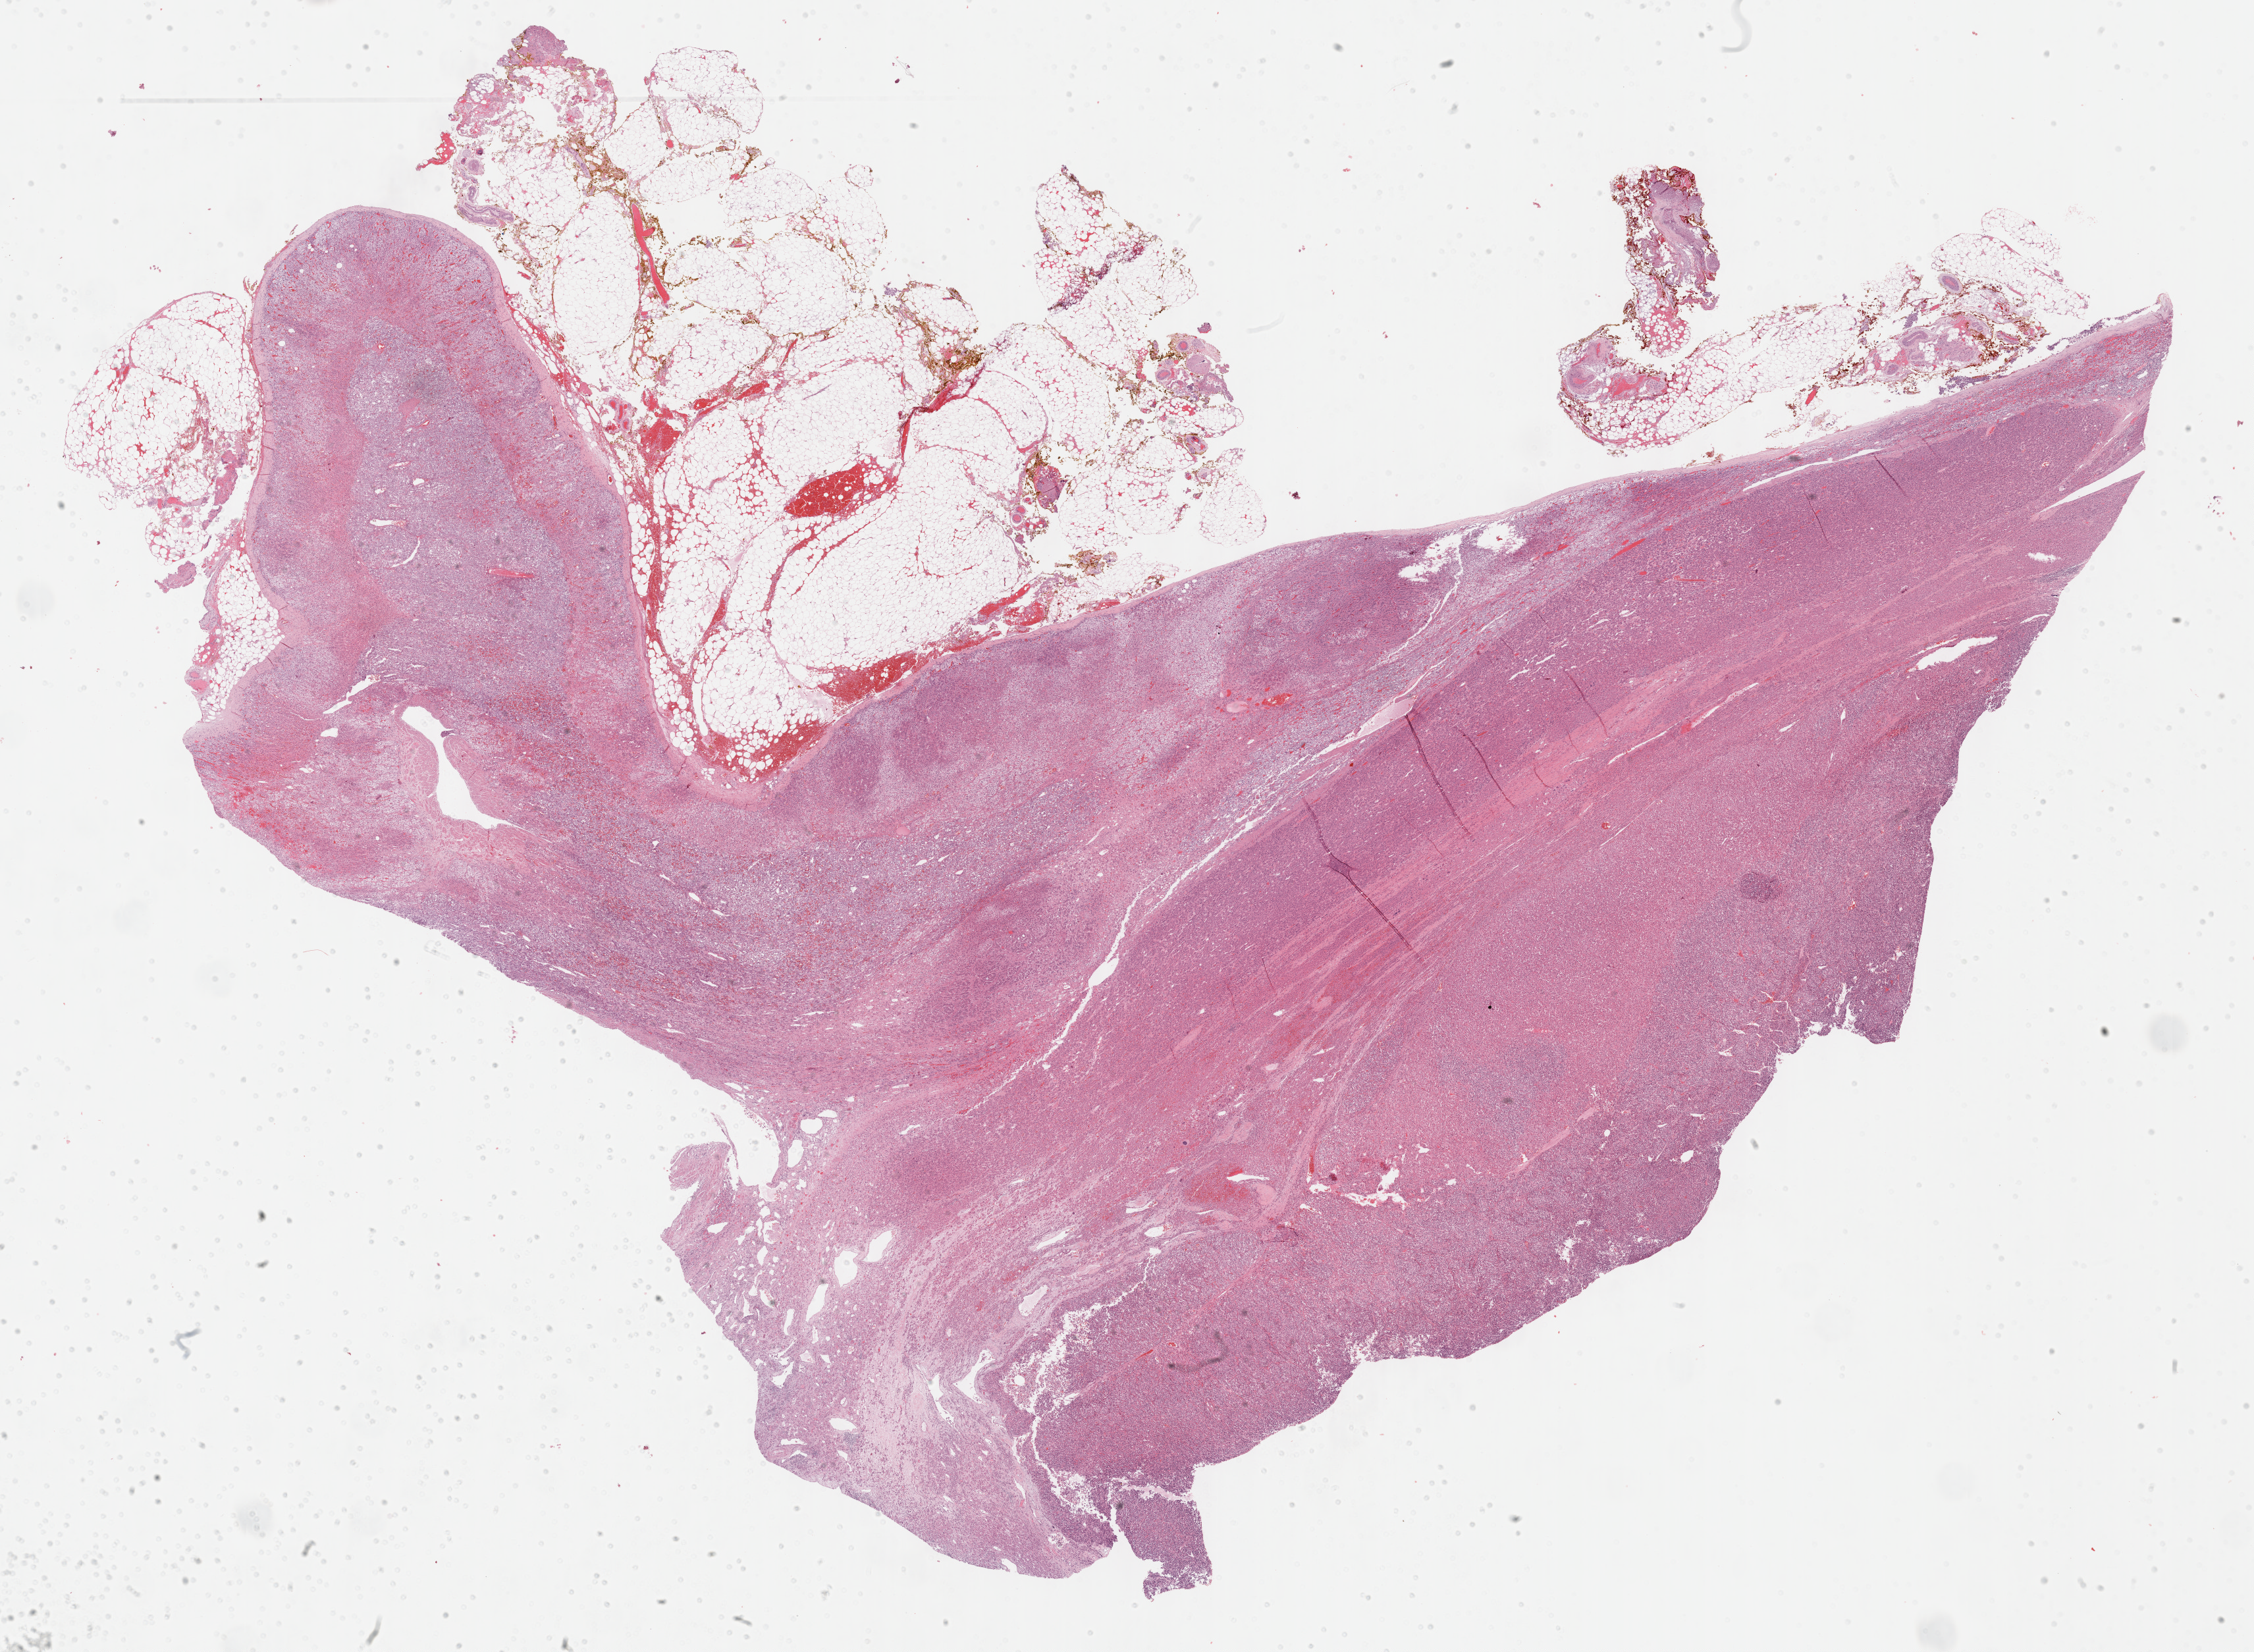
Whole-slide histology image, H&E, low-resolution overview of the scanned area, about 27.7 x 20.3 mm (from a 40x scan), formalin-fixed paraffin-embedded (FFPE) diagnostic section, sample: primary tumour, adrenal cortex. Patient: male, age at initial diagnosis 60 years.
Laterality: left. Diagnosis: Adrenal cortical carcinoma (cortex of adrenal gland).